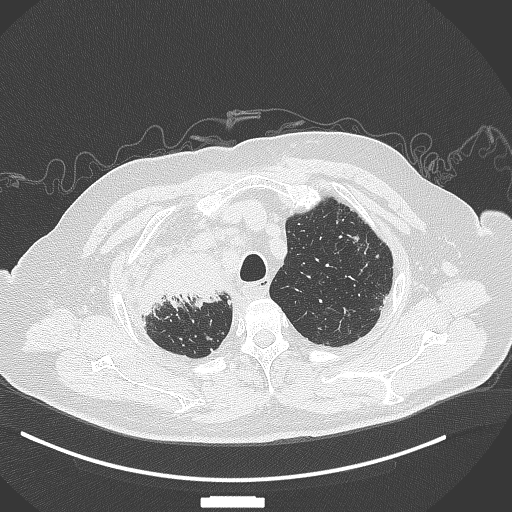
Chest CT, one axial slice. Position 304 of 384 along the scan axis. 120 kVp. Lung window (W 1500 / L -600 HU). 512 × 512 image matrix. Patient: male, 69 years. From the clinical record (not read from this slice): clinical TNM (as recorded): T4 N3 M1.
Outlined on this slice (rectangle marked by the reading radiologist):
- lung tumour (recorded histology: adenocarcinoma): box from (x=136, y=248) to (x=238, y=318) px